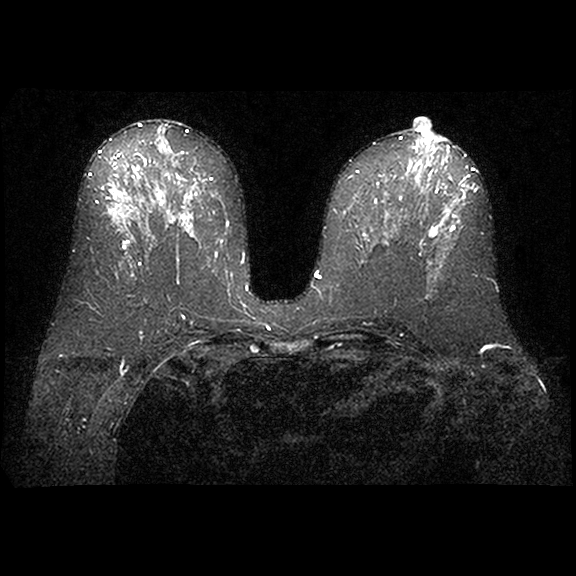
MRI of the breasts; 2 images, each one mid-volume slice chosen by position.
Image 1: axial T2-weighted / STIR image, series "STIR SENSE", slice 44 of 86, 2 mm slice thickness.
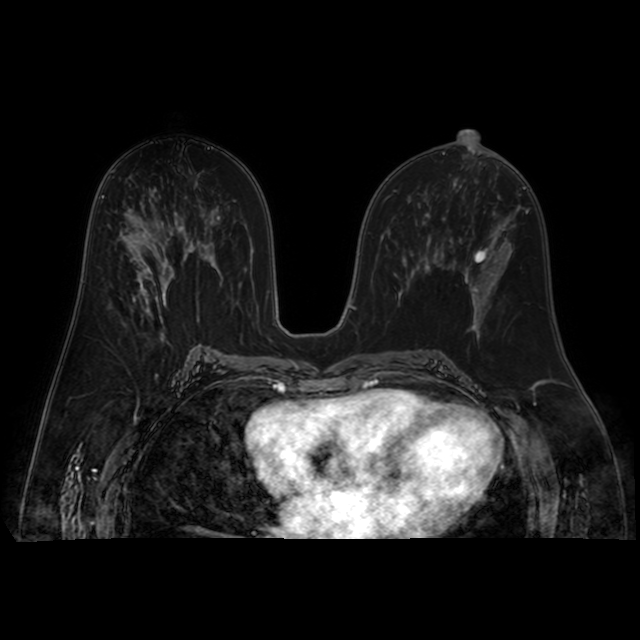
Image 2: axial dynamic contrast-enhanced T1-weighted image, series "AX BLISS_AUTO SENSE", slice 44 of 86, dynamic phase 5 of 8.
Patient-level pathology facts (from the clinical record, not from the images): pathology diagnosis: benign fibrosis (left breast).